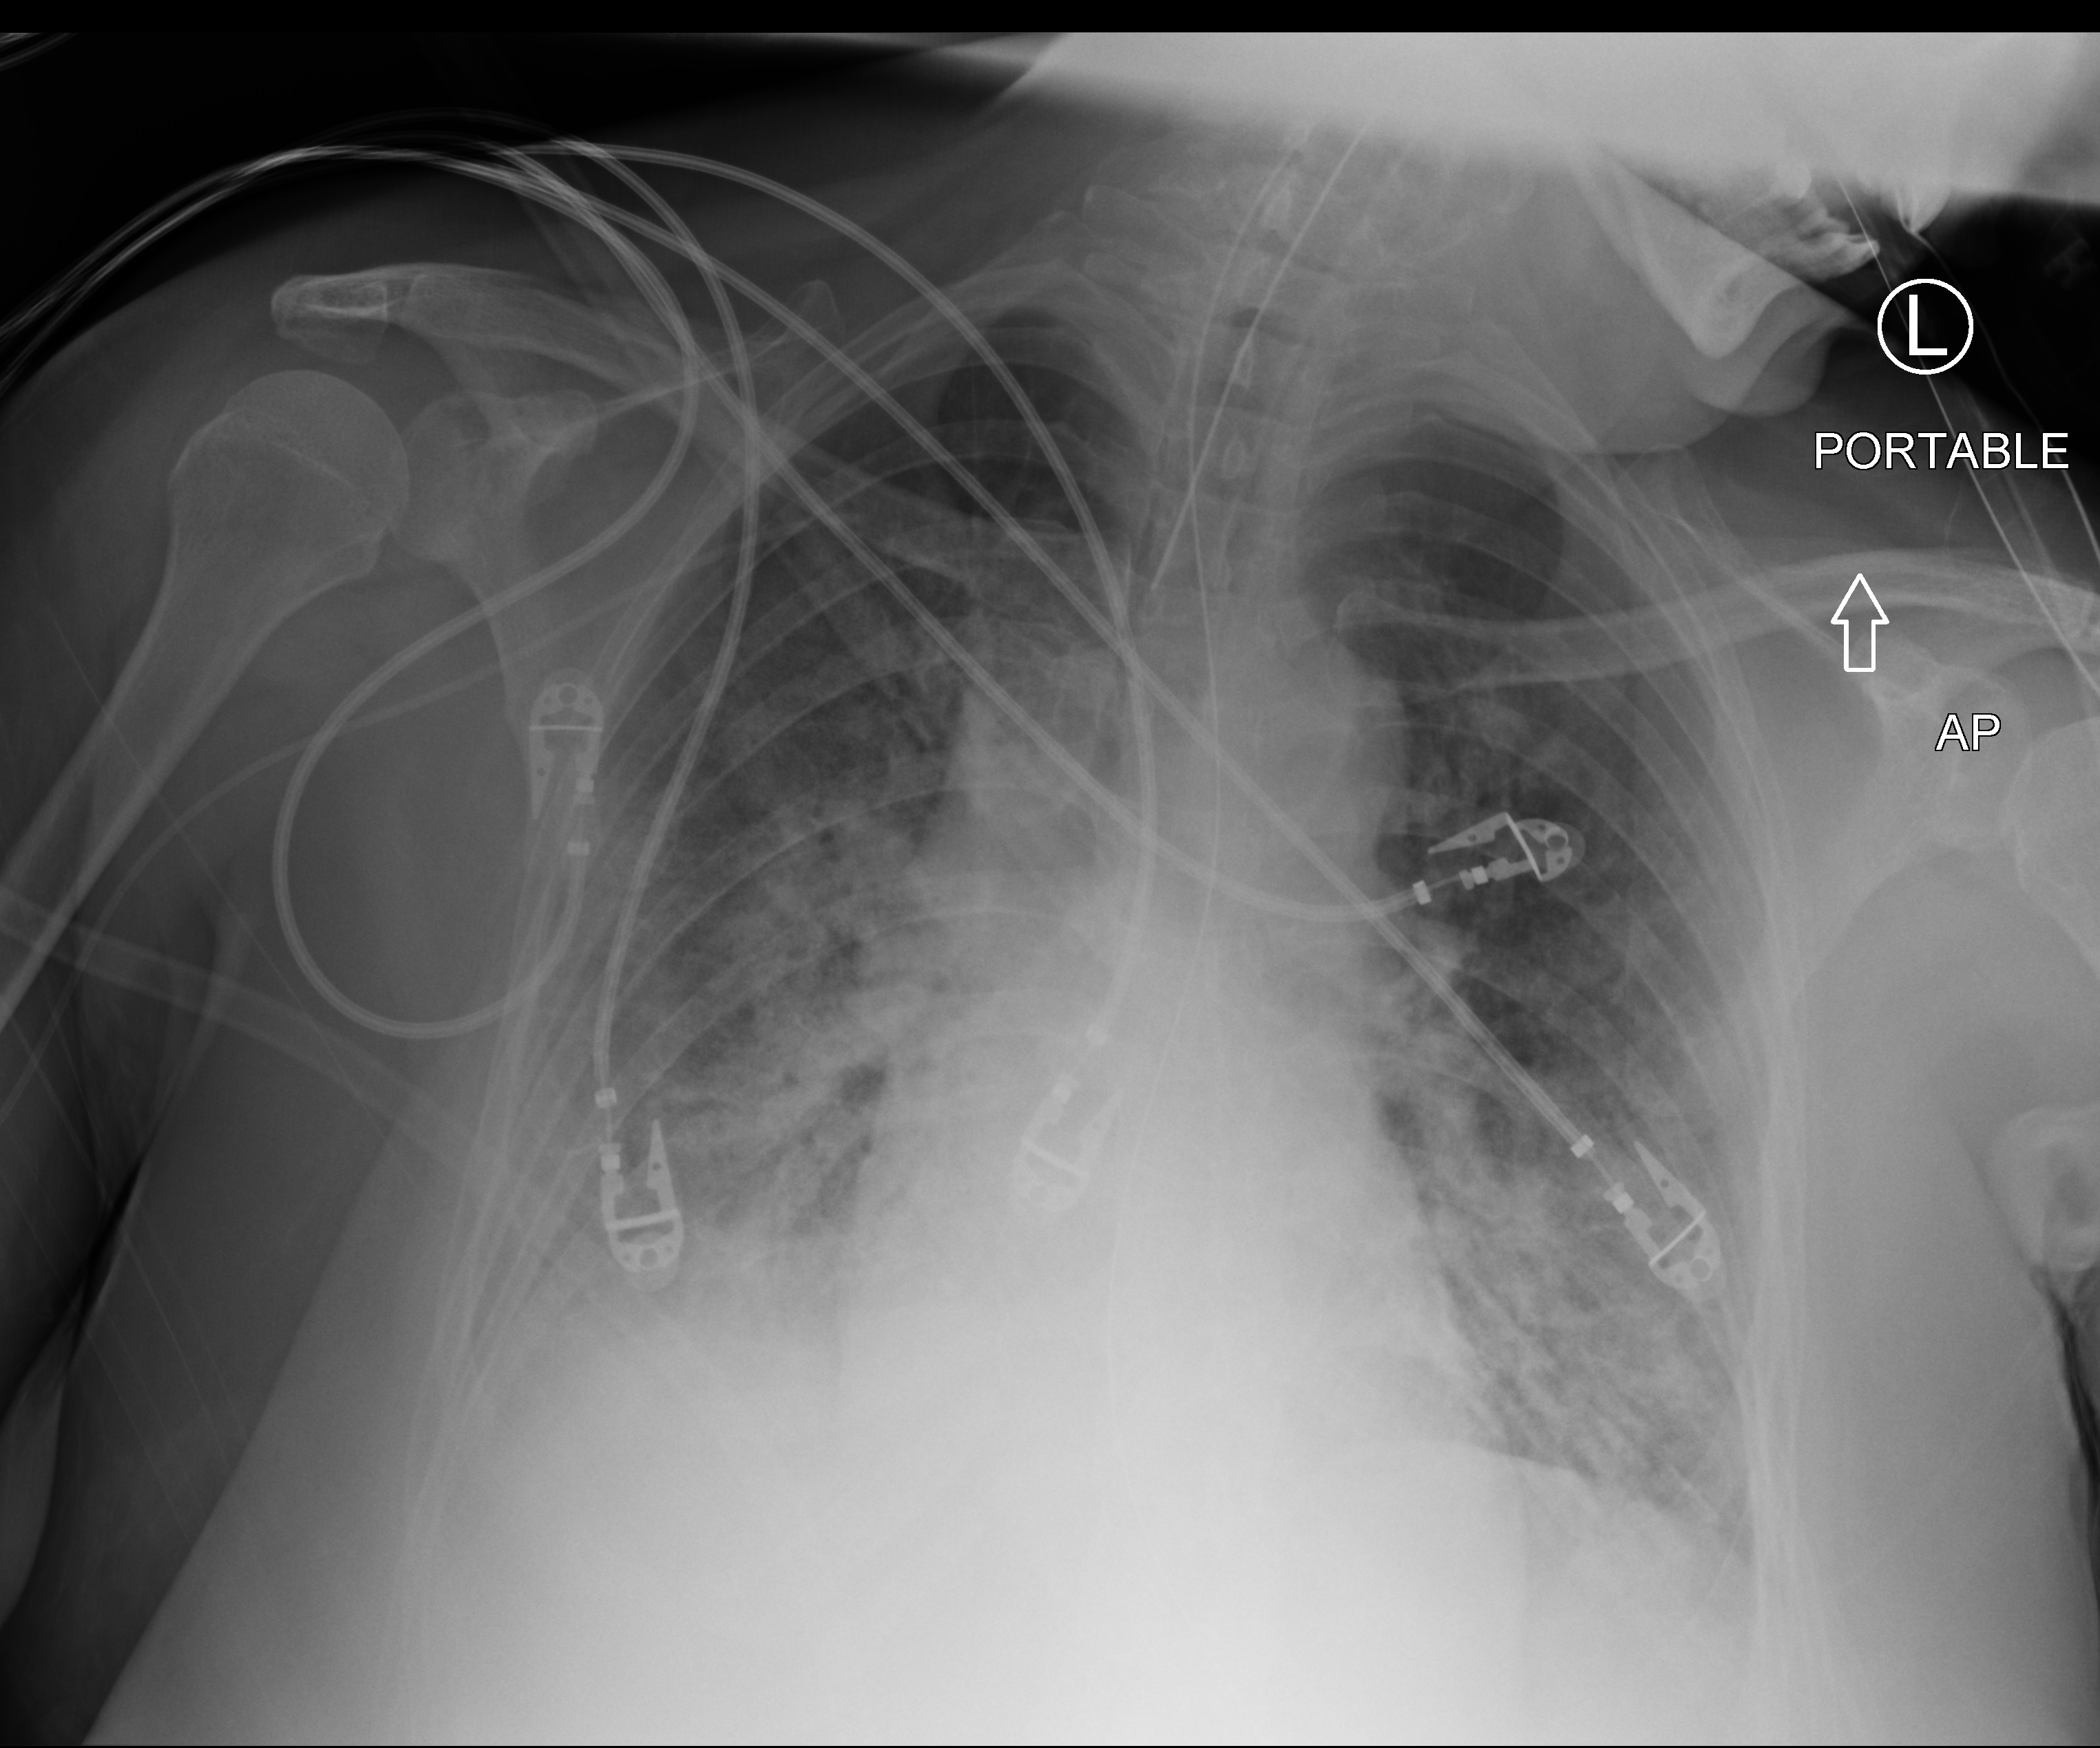
Chest X-ray (portable), anteroposterior (AP) projection. Female patient hospitalised with COVID-19, age 18–59 years.
From the hospital-stay record, not from the radiograph (when in the stay this image was taken is not recorded):
- admitted to intensive care during this hospital stay: yes
- mechanically ventilated during this hospital stay: yes